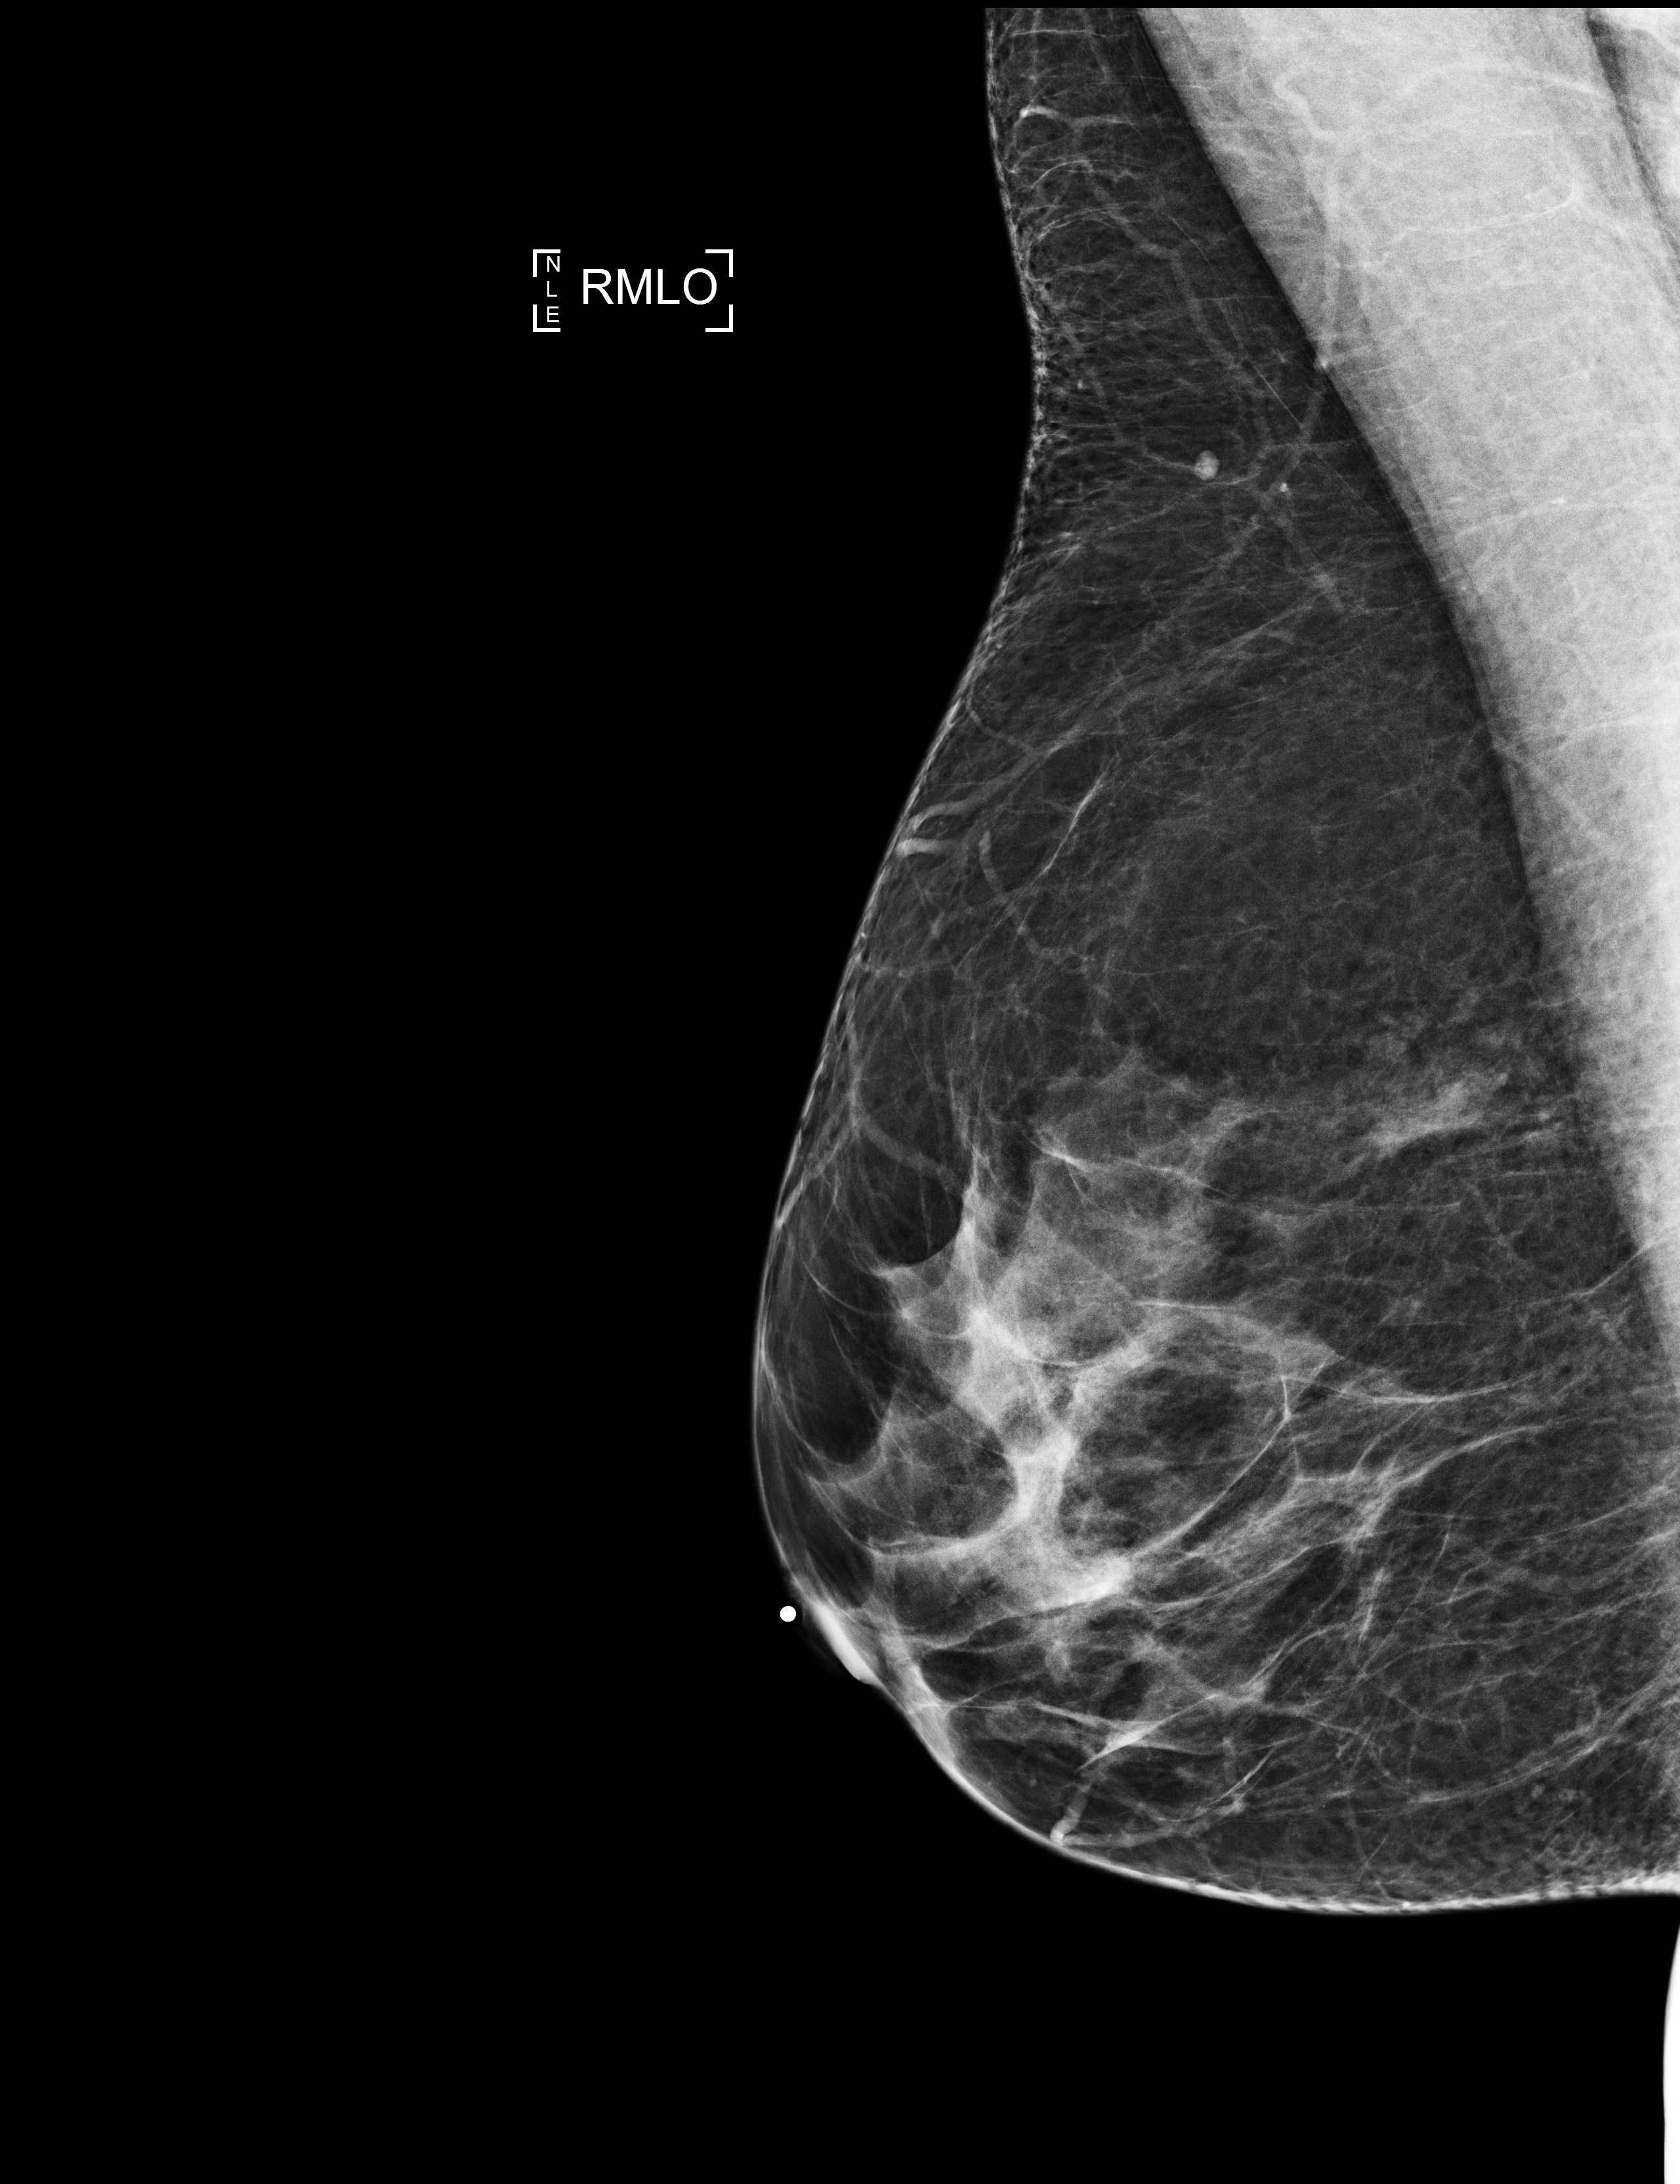
Screening examination; compressed breast thickness 67 mm; system: Selenia Dimensions.
Image type: full-field digital mammogram. Breast: right. Projection: mediolateral oblique (MLO) view.